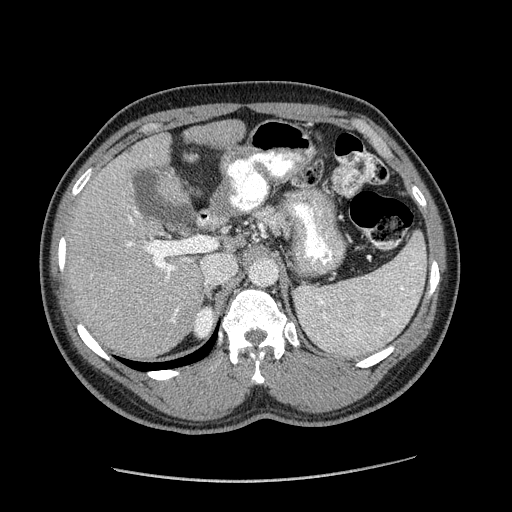
Contrast-enhanced abdominal CT (liver protocol), one axial slice; slice 115 of 182 in the series (ordered by position); 120 kVp; soft-tissue window (W 400 / L 40 HU); 2.5 mm slice thickness; 512 × 512 image matrix, field of view 400 × 400 mm. Case-level facts recorded for this patient, not image findings: diagnosis: hepatocellular carcinoma (patient treated with transarterial chemoembolisation; whether this scan precedes or follows treatment is not stated here); TNM stage (as recorded): Stage-I.
Annotated regions visible in this slice (semi-automatic segmentation, software-assisted and operator-edited):
- liver parenchyma outside the tumour (the mass and vessels are separate outlines, so this box may not span the whole liver): bounding box [x1, y1, x2, y2] px = [66, 120, 246, 358]
- liver vessels: [127, 211, 206, 322]